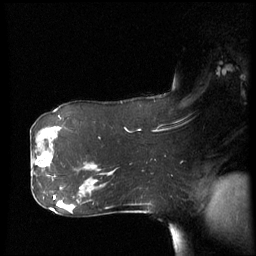
Breast MRI (dynamic contrast-enhanced), one sagittal slice; position 39 of 60 along the scan axis; dynamic contrast-enhanced series, image 2 of 3 at this slice position (ordered by acquisition); 1.5 T; TE 4.2 ms, TR 8.4 ms; 256 × 256 image matrix. Patient: female, 61 years. Case-level facts recorded for this patient, not image findings: setting: breast cancer imaged before/during neoadjuvant chemotherapy; receptor status: HR-positive, HER2-negative.
Annotated regions visible in this slice (semi-automatically segmented with operator editing):
- analysis volume of interest (the breast-tissue region the enhancement analysis was run in; not a lesion): bounding box (x1, y1, x2, y2) in pixels: (32, 142, 57, 179)
- tumour enhancement mask (voxels above the 70 % enhancement threshold inside the analysis volume of interest): (37, 158, 51, 167)